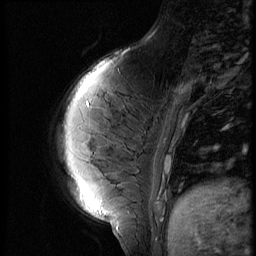
Breast MRI (dynamic contrast-enhanced), one sagittal slice. Position 16 of 56 along the scan axis. 3 images stored at this slice position (order not interpretable as contrast timing). 1.5 T. TE 4.2 ms, TR 9 ms. 2.5 mm slice thickness. 256 × 256 image matrix, field of view 180 × 180 mm. Female patient, age 35 years. Case-level facts recorded for this patient, not image findings: setting: breast cancer imaged before/during neoadjuvant chemotherapy; receptor status: HR-positive, HER2-negative.
Structures marked on this image (semi-automatically segmented with operator editing):
- analysis volume of interest (the breast-tissue region the enhancement analysis was run in; not a lesion): bounding box [x1, y1, x2, y2] px = [58, 70, 171, 208]
- tumour enhancement mask (voxels above the 140 % enhancement threshold inside the analysis volume of interest): [166, 158, 170, 173]